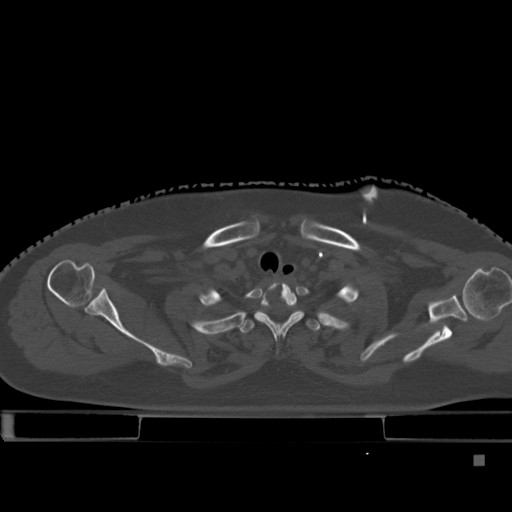
CT including the spine, one axial slice. Position 367 of 495 along the scan axis. Bone window (W 1800 / L 400 HU). 512 × 512 image matrix. Female patient, age 33 years. From the clinical record (not read from this slice): primary cancer: breast; vertebrae with lytic lesions (as recorded): T1.
Outlined on this slice (semi-automatically segmented with operator editing):
- T1 vertebra: bounding box [x1, y1, x2, y2] px = [258, 282, 303, 337]
- T2 vertebra: [238, 310, 342, 334]